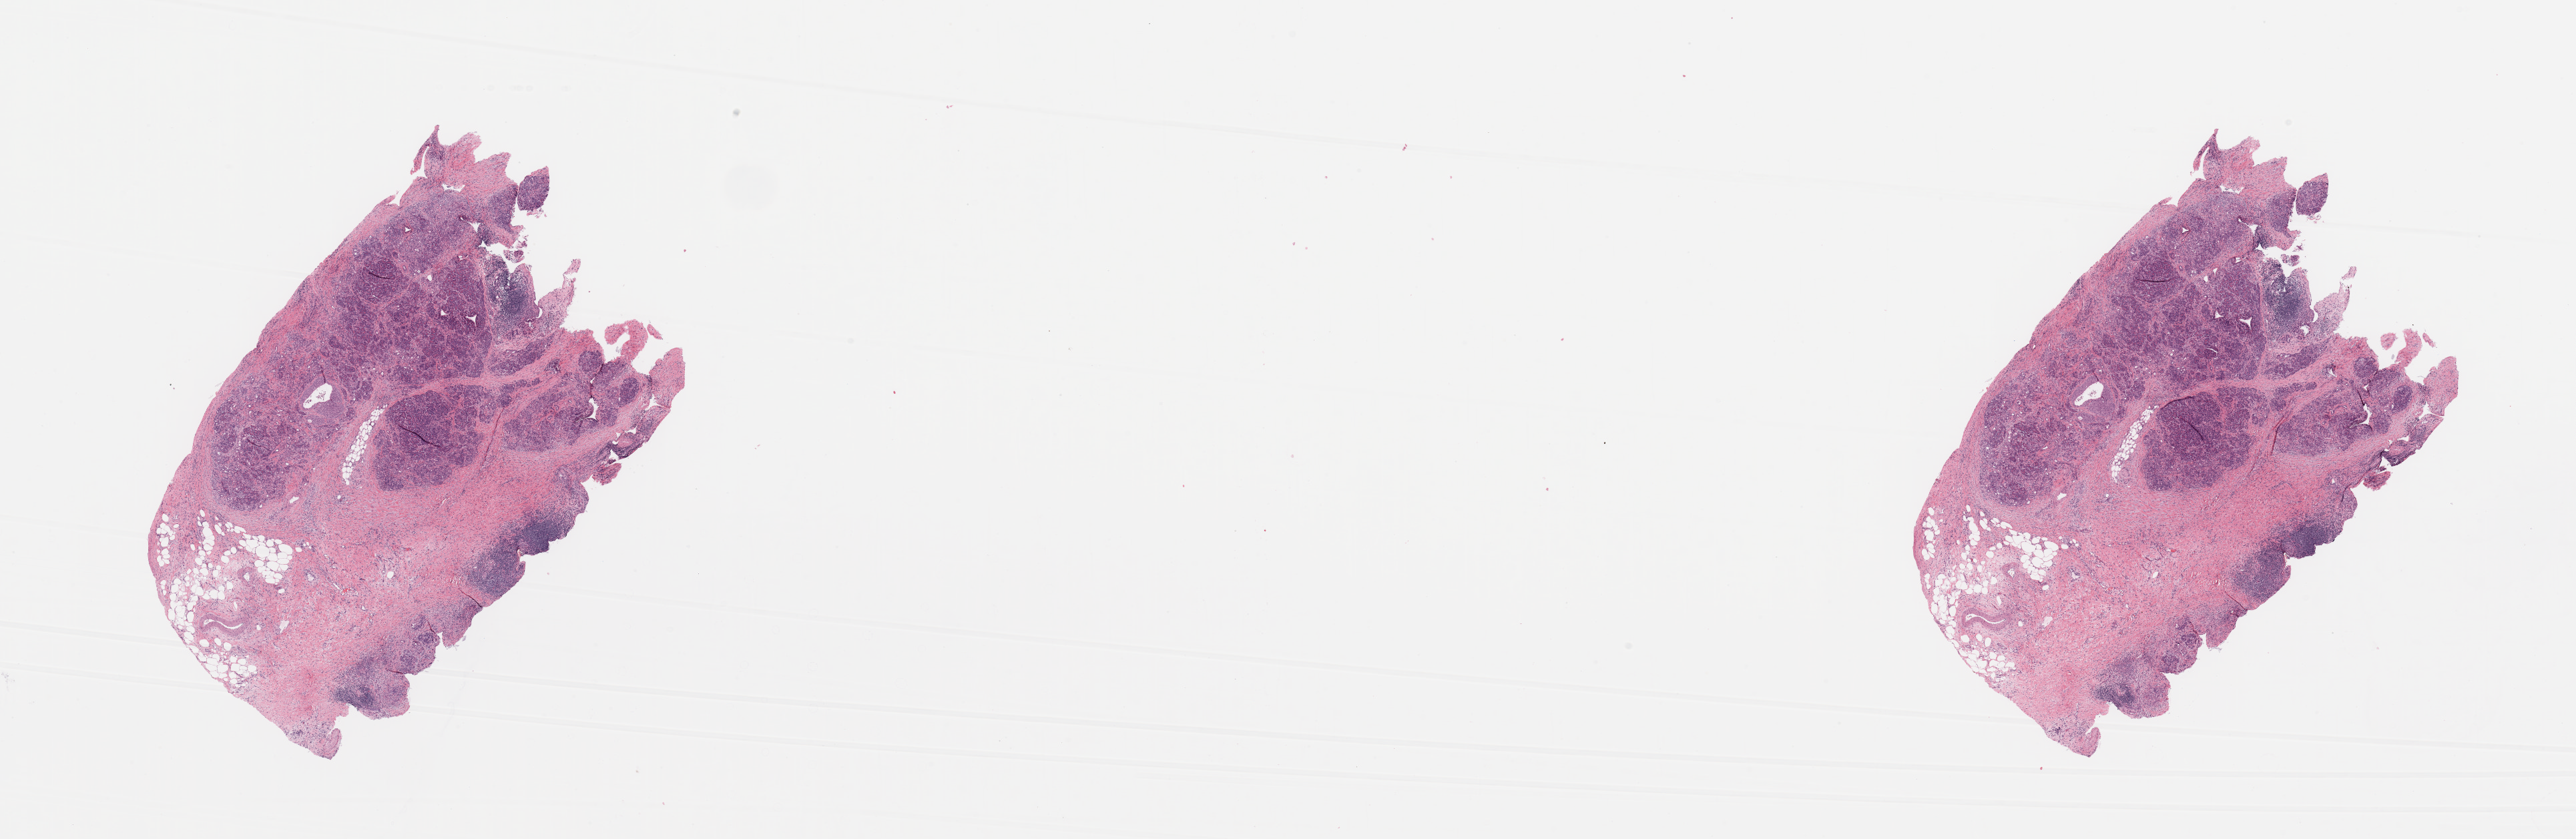
Digitized H&E tissue section (whole slide), whole scanned area (about 30.5 x 9.9 mm) shown as a low-resolution overview, tumour tissue sample, pancreas. 68-year-old male patient.
• primary tumour site (as recorded): tail
• patient diagnosis (cohort enrolment): ductal adenocarcinoma (pancreas)